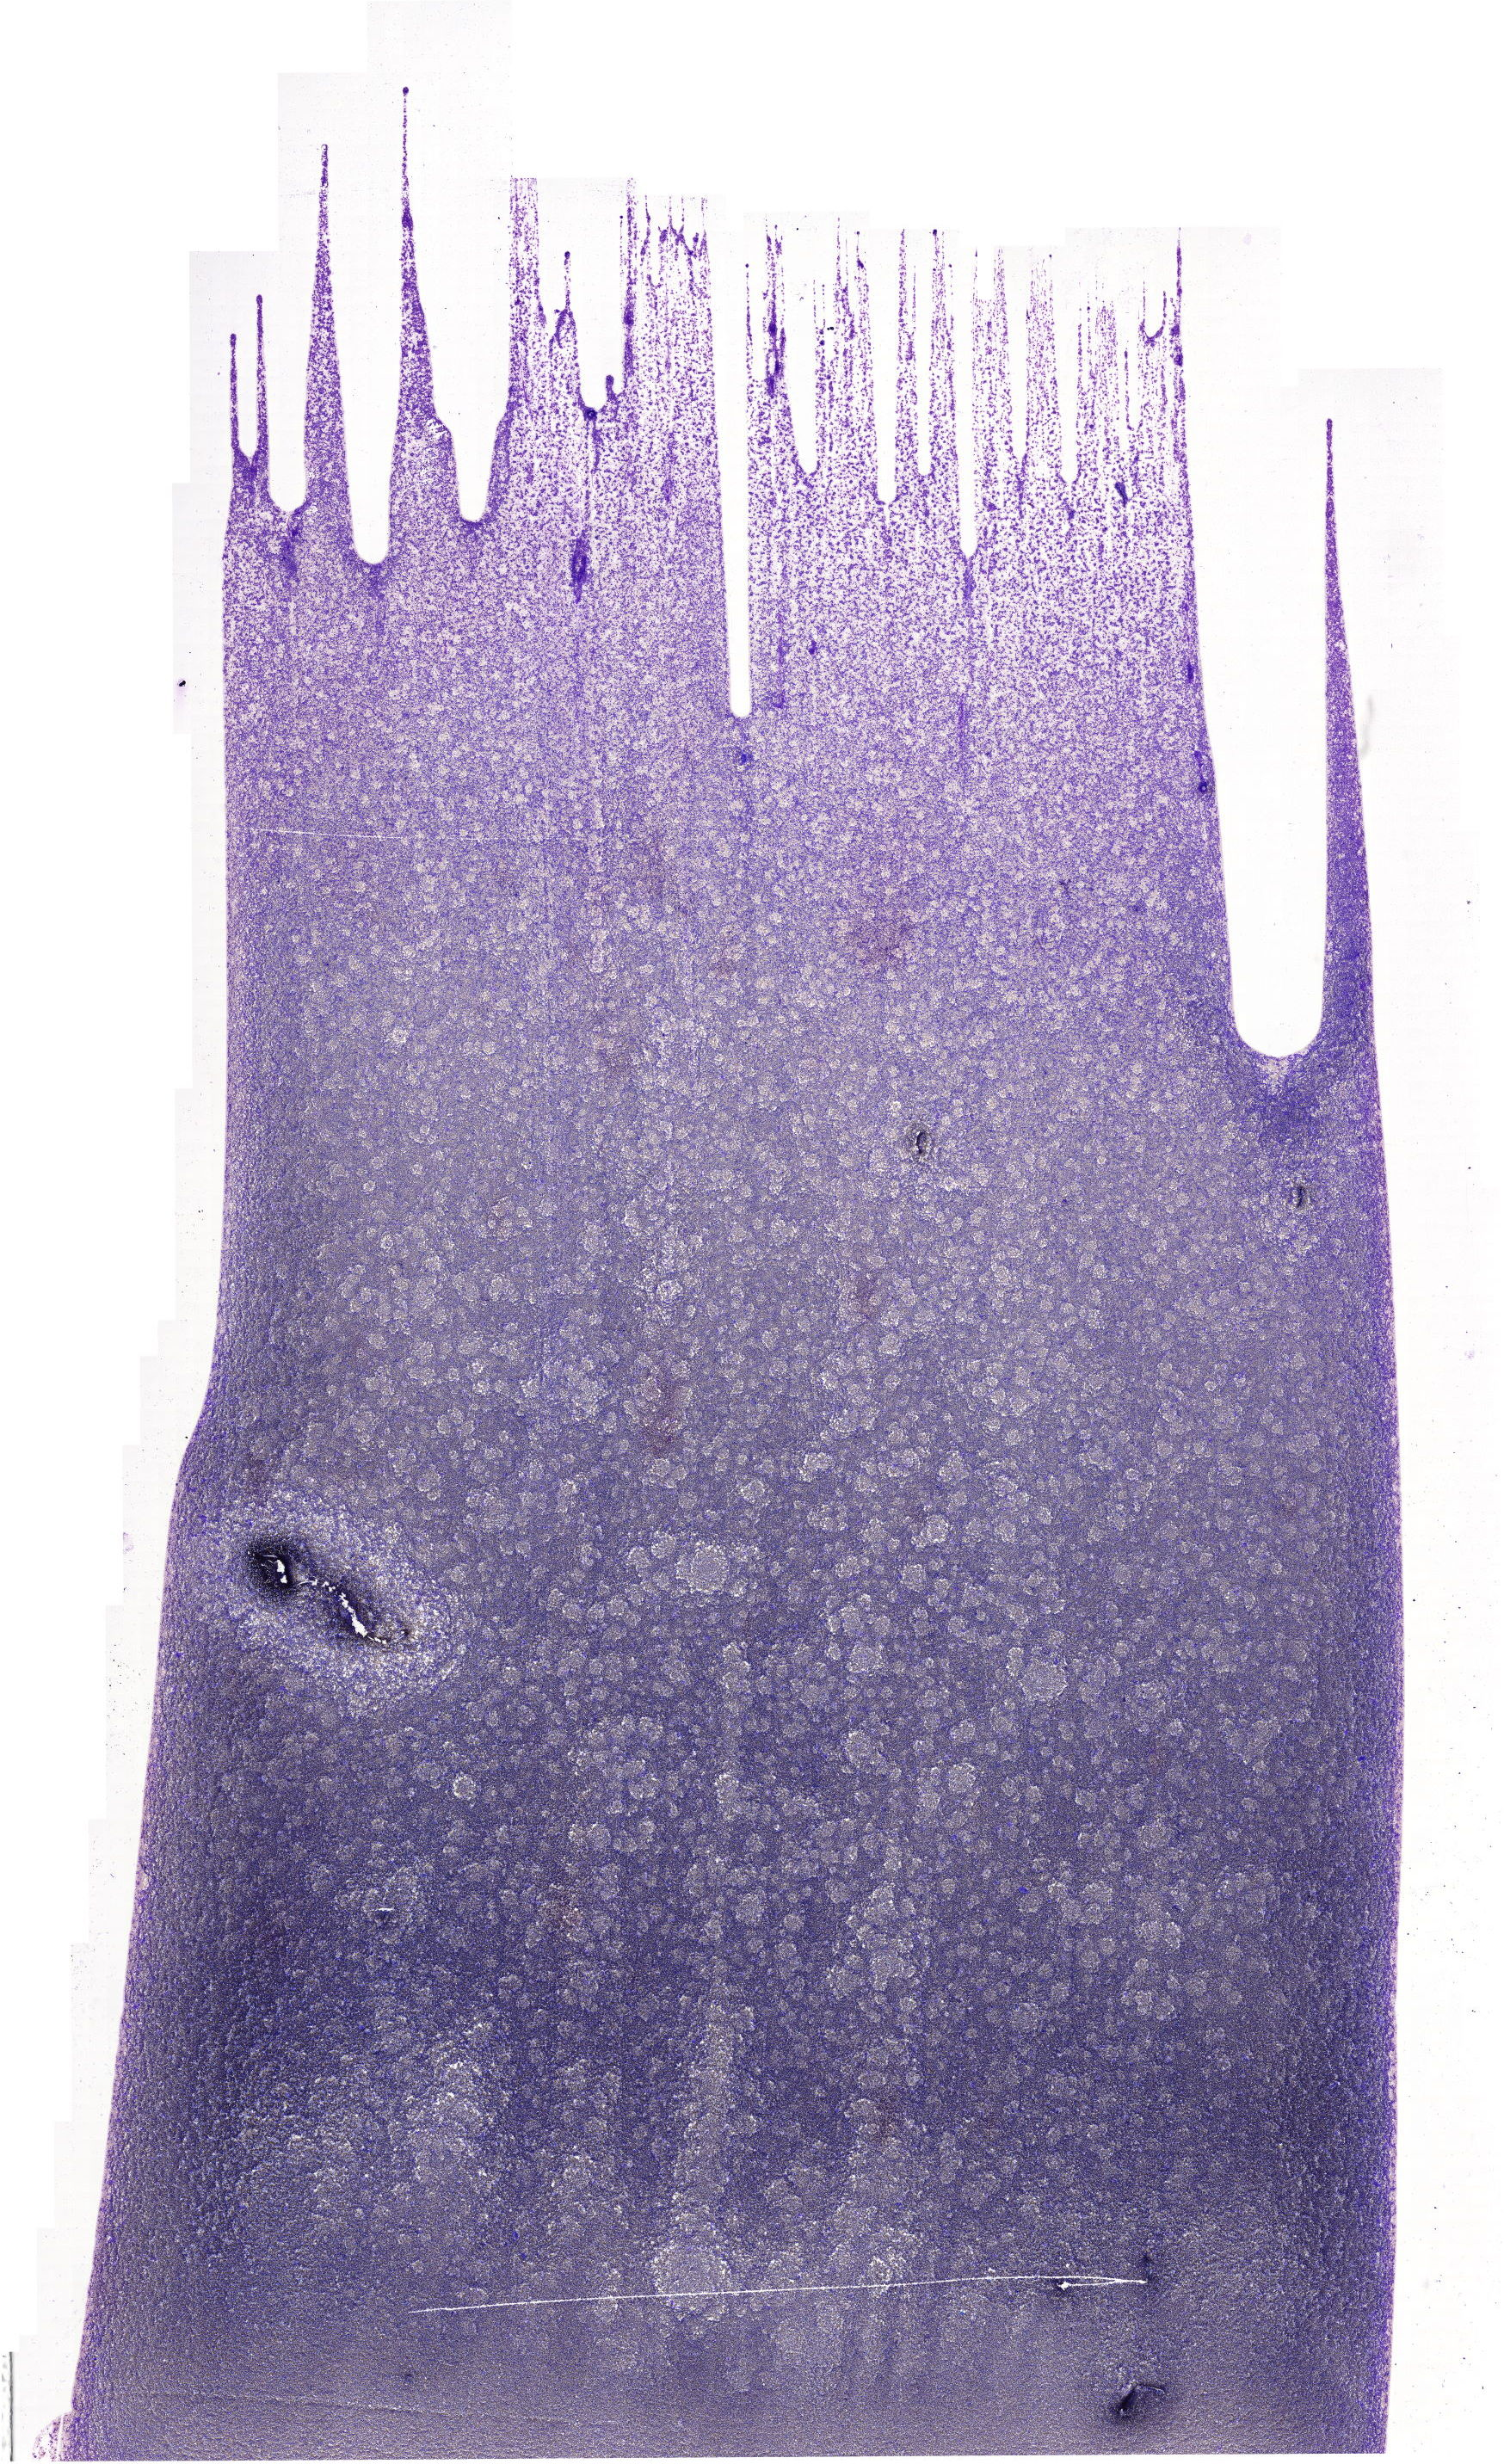
May-Grünwald–Giemsa-stained marrow aspirate smear (whole slide) — low-resolution overview of the scanned area, about 21.8 x 35.6 mm. Male patient.
Diagnosis: Chronic Phase Chronic Myeloid Leukemia, BCR-ABL1 Positive.